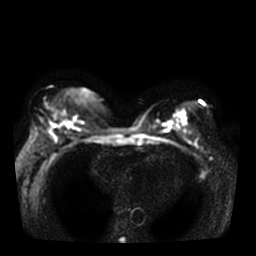
Breast MRI, one axial slice. Slice 16 of 36 in the series (ordered by position). Diffusion-weighted series; image 2 of 4 stored at this slice position (different b-values; order by instance number). 3 T. 5 mm slice thickness. 256 × 256 image matrix, field of view 330 × 330 mm. Female patient.
Structures marked on this image (outlined manually by an expert reader):
- tumour on diffusion-weighted imaging: bounding box [x1, y1, x2, y2] px = [65, 121, 73, 127]